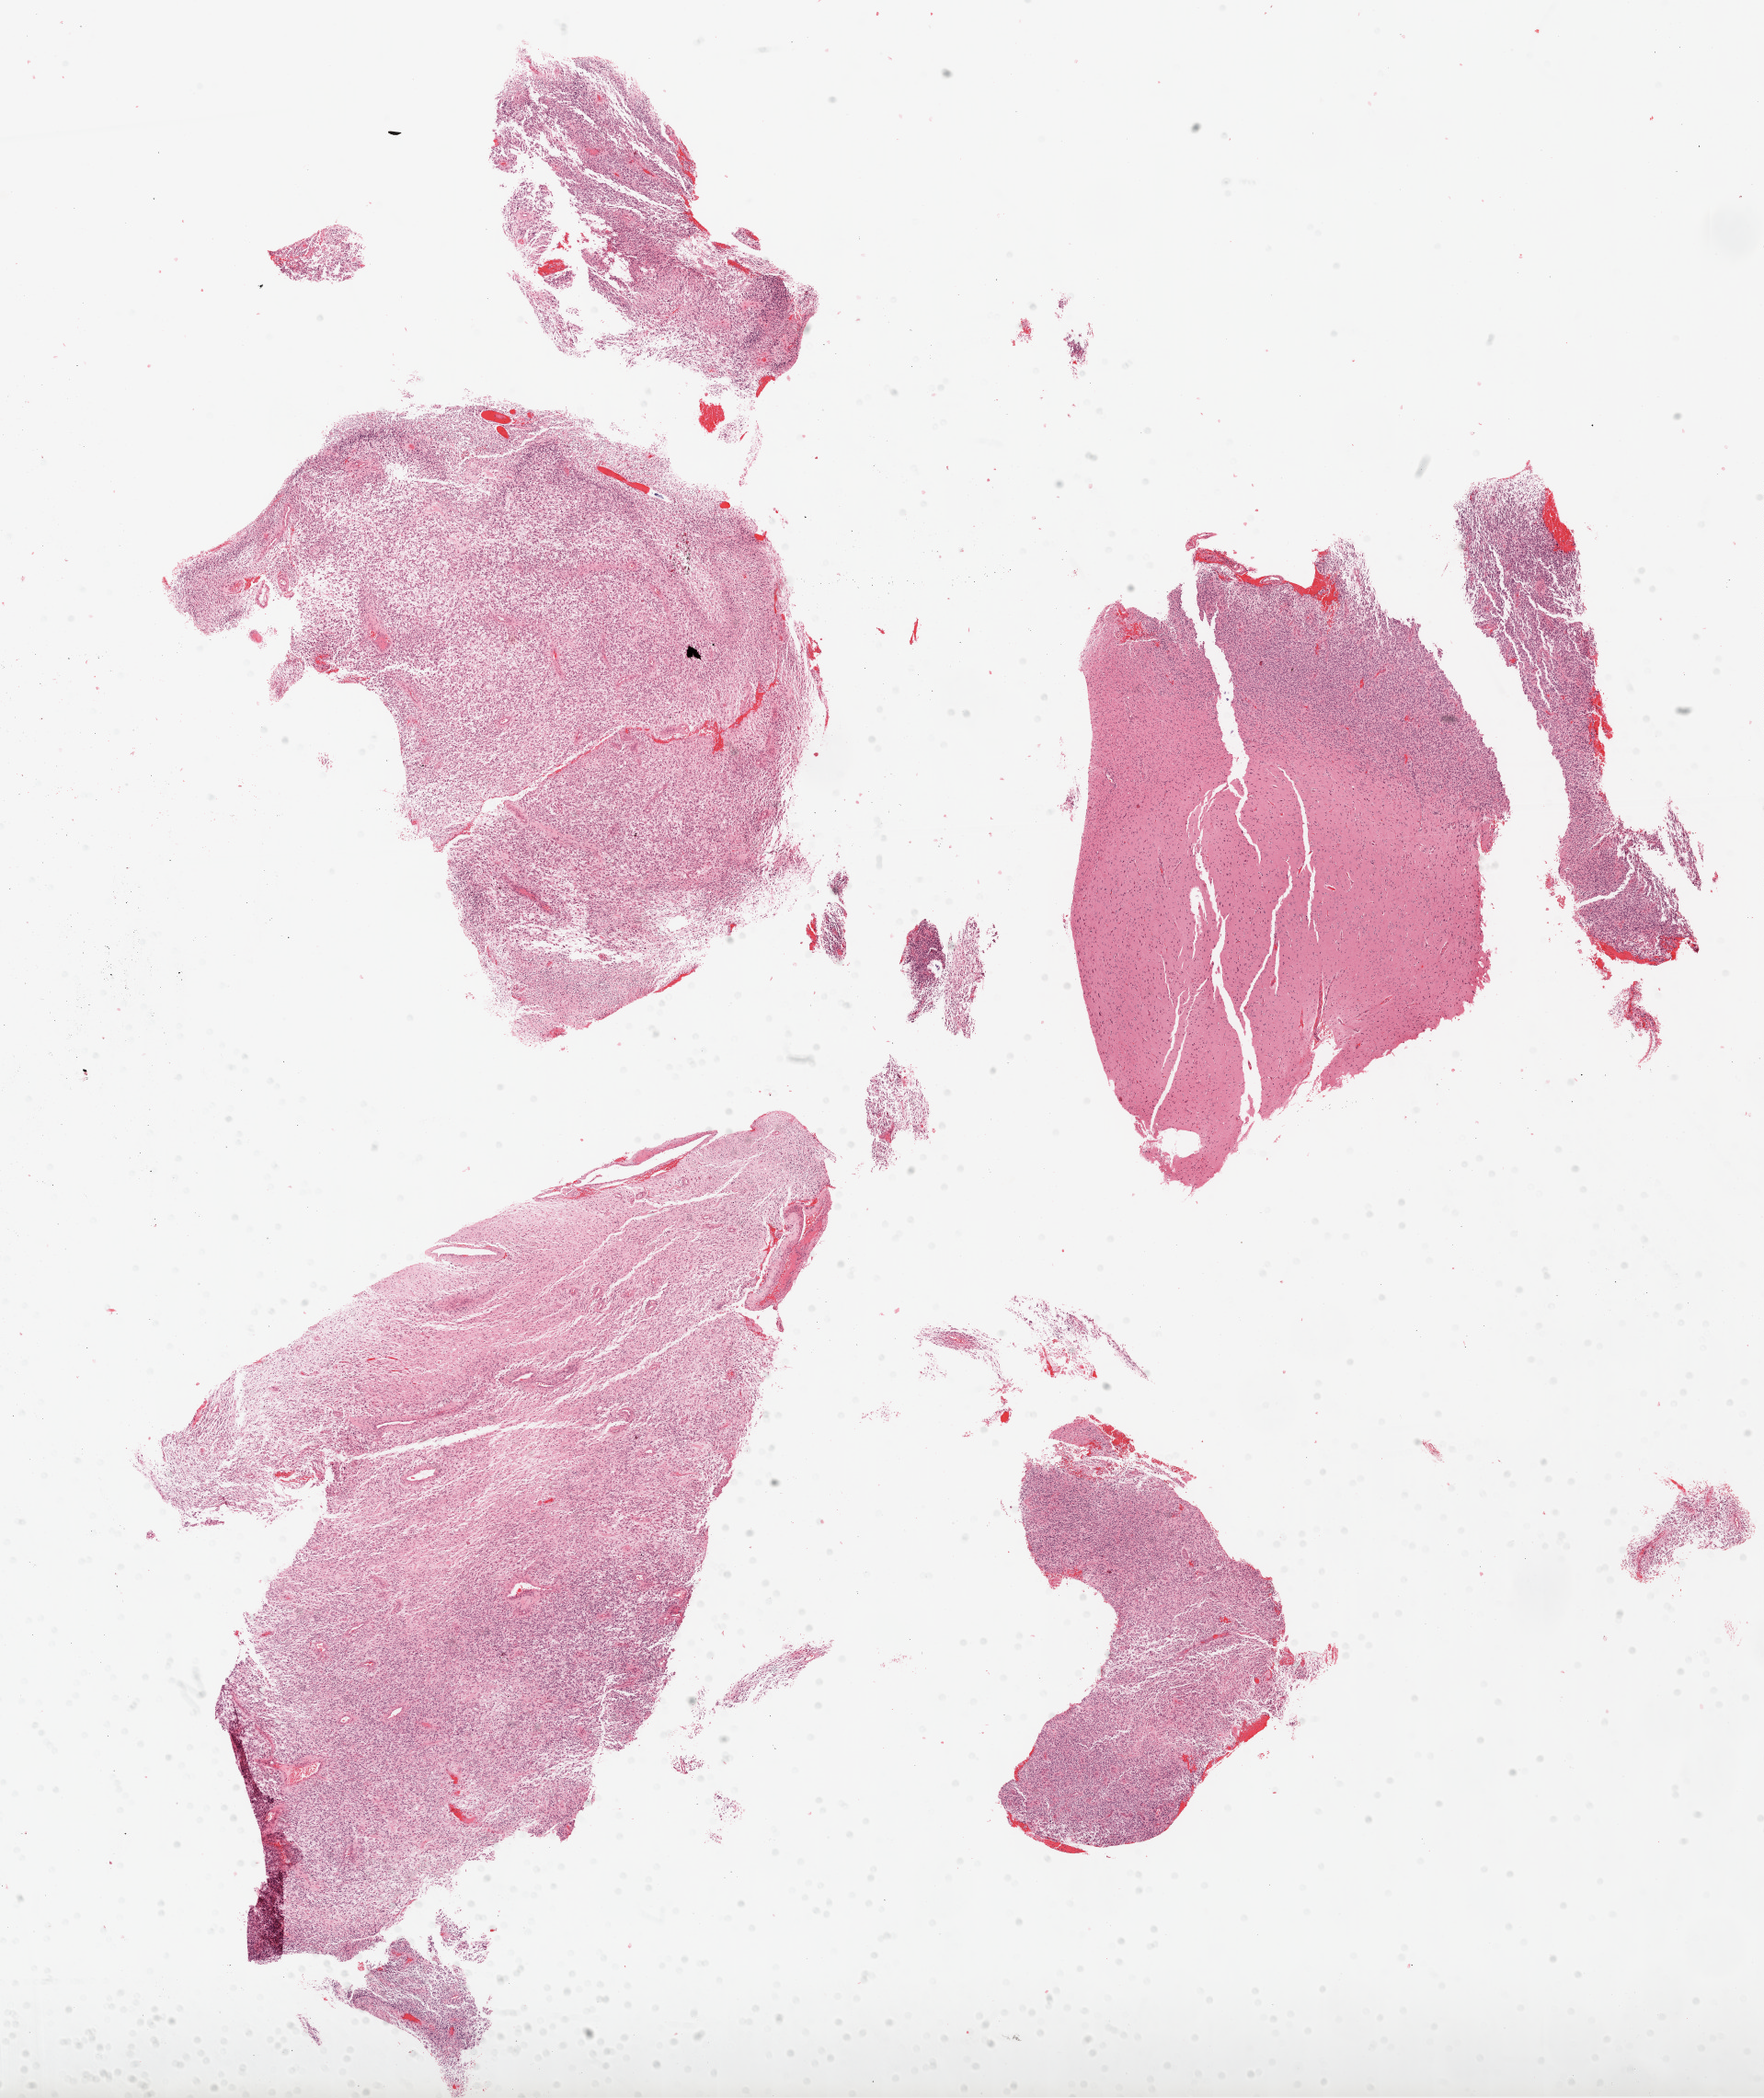
H&E-stained whole-slide image, whole scanned area (about 15.5 x 18.4 mm, slide scanned at 20x) shown as a low-resolution overview. Formalin-fixed paraffin-embedded (FFPE) diagnostic section. Brain, primary tumour sample. Patient: male, age at initial diagnosis 65 years.
Histologic diagnosis: Glioblastoma.